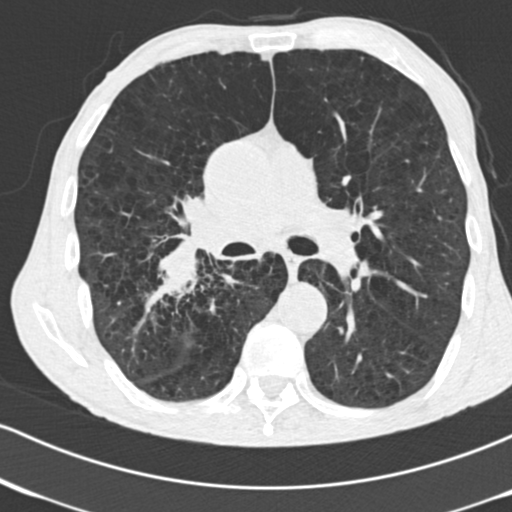
Low-dose screening chest CT, one axial slice. Slice 99 of 182 in the series (ordered by position). Reconstruction kernel B30f. 120 kVp. Lung window (W 1500 / L -600 HU). 512 × 512 image matrix, field of view 316 × 316 mm.
Outlined on this slice (manually delineated by an expert):
- lesion 1 (tumor, lower lobe of right lung): bounding box <158,242,202,297> (left, top, right, bottom; pixels)